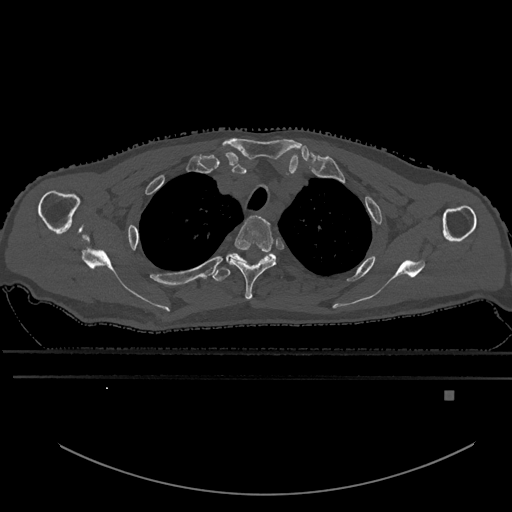
CT including the spine, one axial slice. Slice 484 of 969 in the series (ordered by position). Bone window (W 1800 / L 400 HU). 512 × 512 image matrix. Patient: male, 82 years. From the clinical record (not read from this slice): primary cancer: prostate; vertebrae with lytic lesions (as recorded): T11, T9, T8, T2.
Structures marked on this image (semi-automatic segmentation, software-assisted and operator-edited):
- T2 vertebra: bounding box <227,215,277,300> (left, top, right, bottom; pixels)
- T3 vertebra: <212,253,284,282>